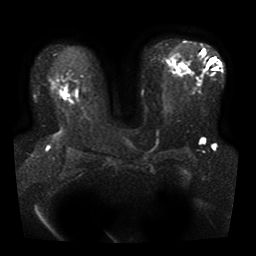
Breast MRI, one axial slice; slice 22 of 41 in the series (ordered by position); diffusion-weighted series; image 2 of 4 stored at this slice position (different b-values; order by instance number); 1.5 T; 256 × 256 image matrix, field of view 330 × 330 mm. Female patient.
Annotated regions visible in this slice (outlined manually by an expert reader):
- tumour on diffusion-weighted imaging: bounding box <61,92,68,96> (left, top, right, bottom; pixels)